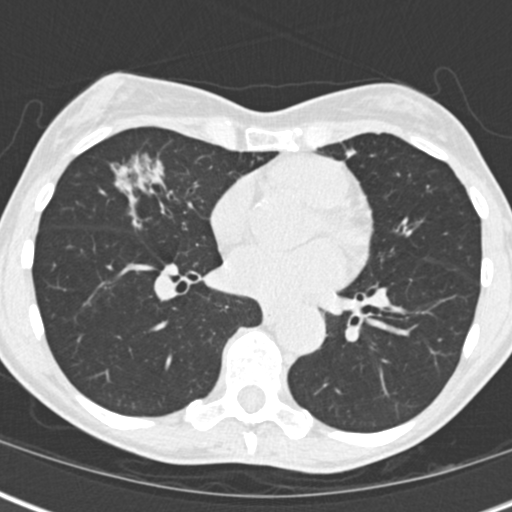
Low-dose screening chest CT, one axial slice. Position 76 of 173 along the scan axis. Reconstruction kernel B30f. 120 kVp. Lung window (W 1500 / L -600 HU). 2 mm slice thickness. 512 × 512 image matrix.
Annotated regions visible in this slice (expert manual segmentation):
- lesion 1 (tumor, middle lobe of right lung): bounding box (x1, y1, x2, y2) in pixels: (118, 162, 158, 189)